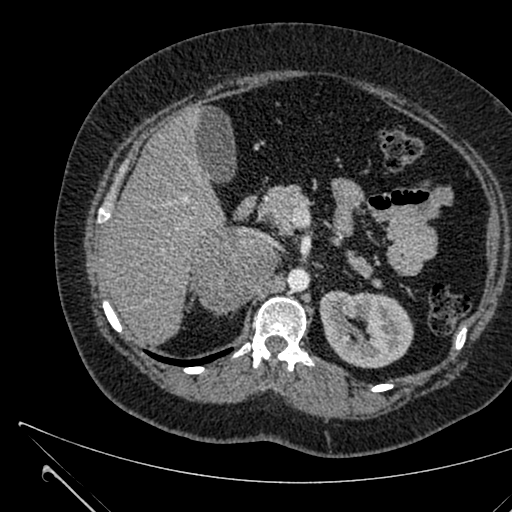
Contrast-enhanced abdominal CT, one axial slice; 120 kVp; soft-tissue window (W 400 / L 40 HU); 512 × 512 image matrix, field of view 376 × 376 mm. Female patient, age 36 years. Case-level facts recorded for this patient, not image findings: diagnosis: adrenocortical carcinoma; tumour side: right adrenal; tumour size at pathology: 10 cm; Ki-67 index: 20 %; stage (as recorded): 4.
Outlined on this slice (semi-automatically segmented with operator editing):
- mass: bounding box (x1, y1, x2, y2) in pixels: (196, 229, 272, 313)